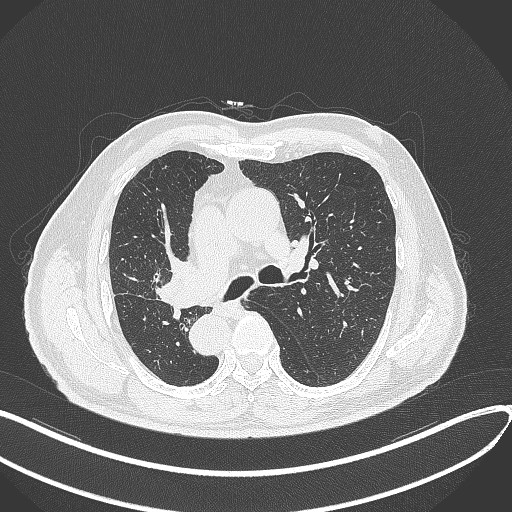
Chest CT, one axial slice; position 183 of 300 along the scan axis; reconstruction kernel B70f; lung window (W 1500 / L -600 HU); 1 mm slice thickness; 512 × 512 image matrix. Patient: male, 67 years. From the clinical record (not read from this slice): clinical TNM (as recorded): T2a N0 M0.
Structures marked on this image (bounding box drawn by a radiologist):
- lung tumour (recorded histology: squamous cell carcinoma): box from (x=154, y=252) to (x=208, y=312) px